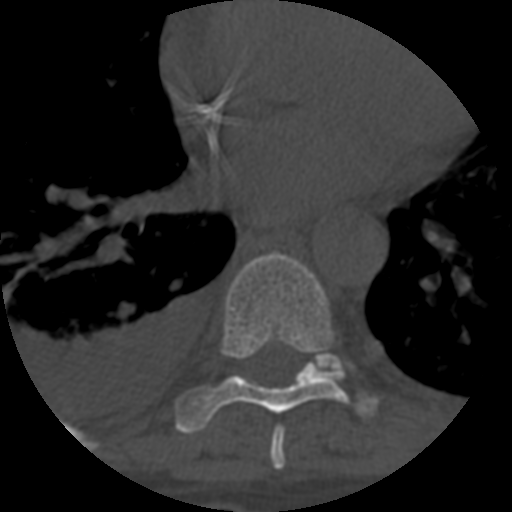
CT including the spine, one axial slice. Position 396 of 708 along the scan axis. Reconstruction kernel STANDARD. 120 kVp. One of 3 acquisitions stored at this slice position. Bone window (W 1800 / L 400 HU). 1.25 mm slice thickness. 512 × 512 image matrix. Patient age 55 years. From the clinical record (not read from this slice): primary cancer: colon; vertebrae with lytic lesions (as recorded): T12, L1, L5.
Annotated regions visible in this slice (semi-automatically segmented with operator editing):
- T7 vertebra: bounding box <270,427,286,467> (left, top, right, bottom; pixels)
- T8 vertebra: <175,253,377,434>
- T9 vertebra: <312,353,343,371>